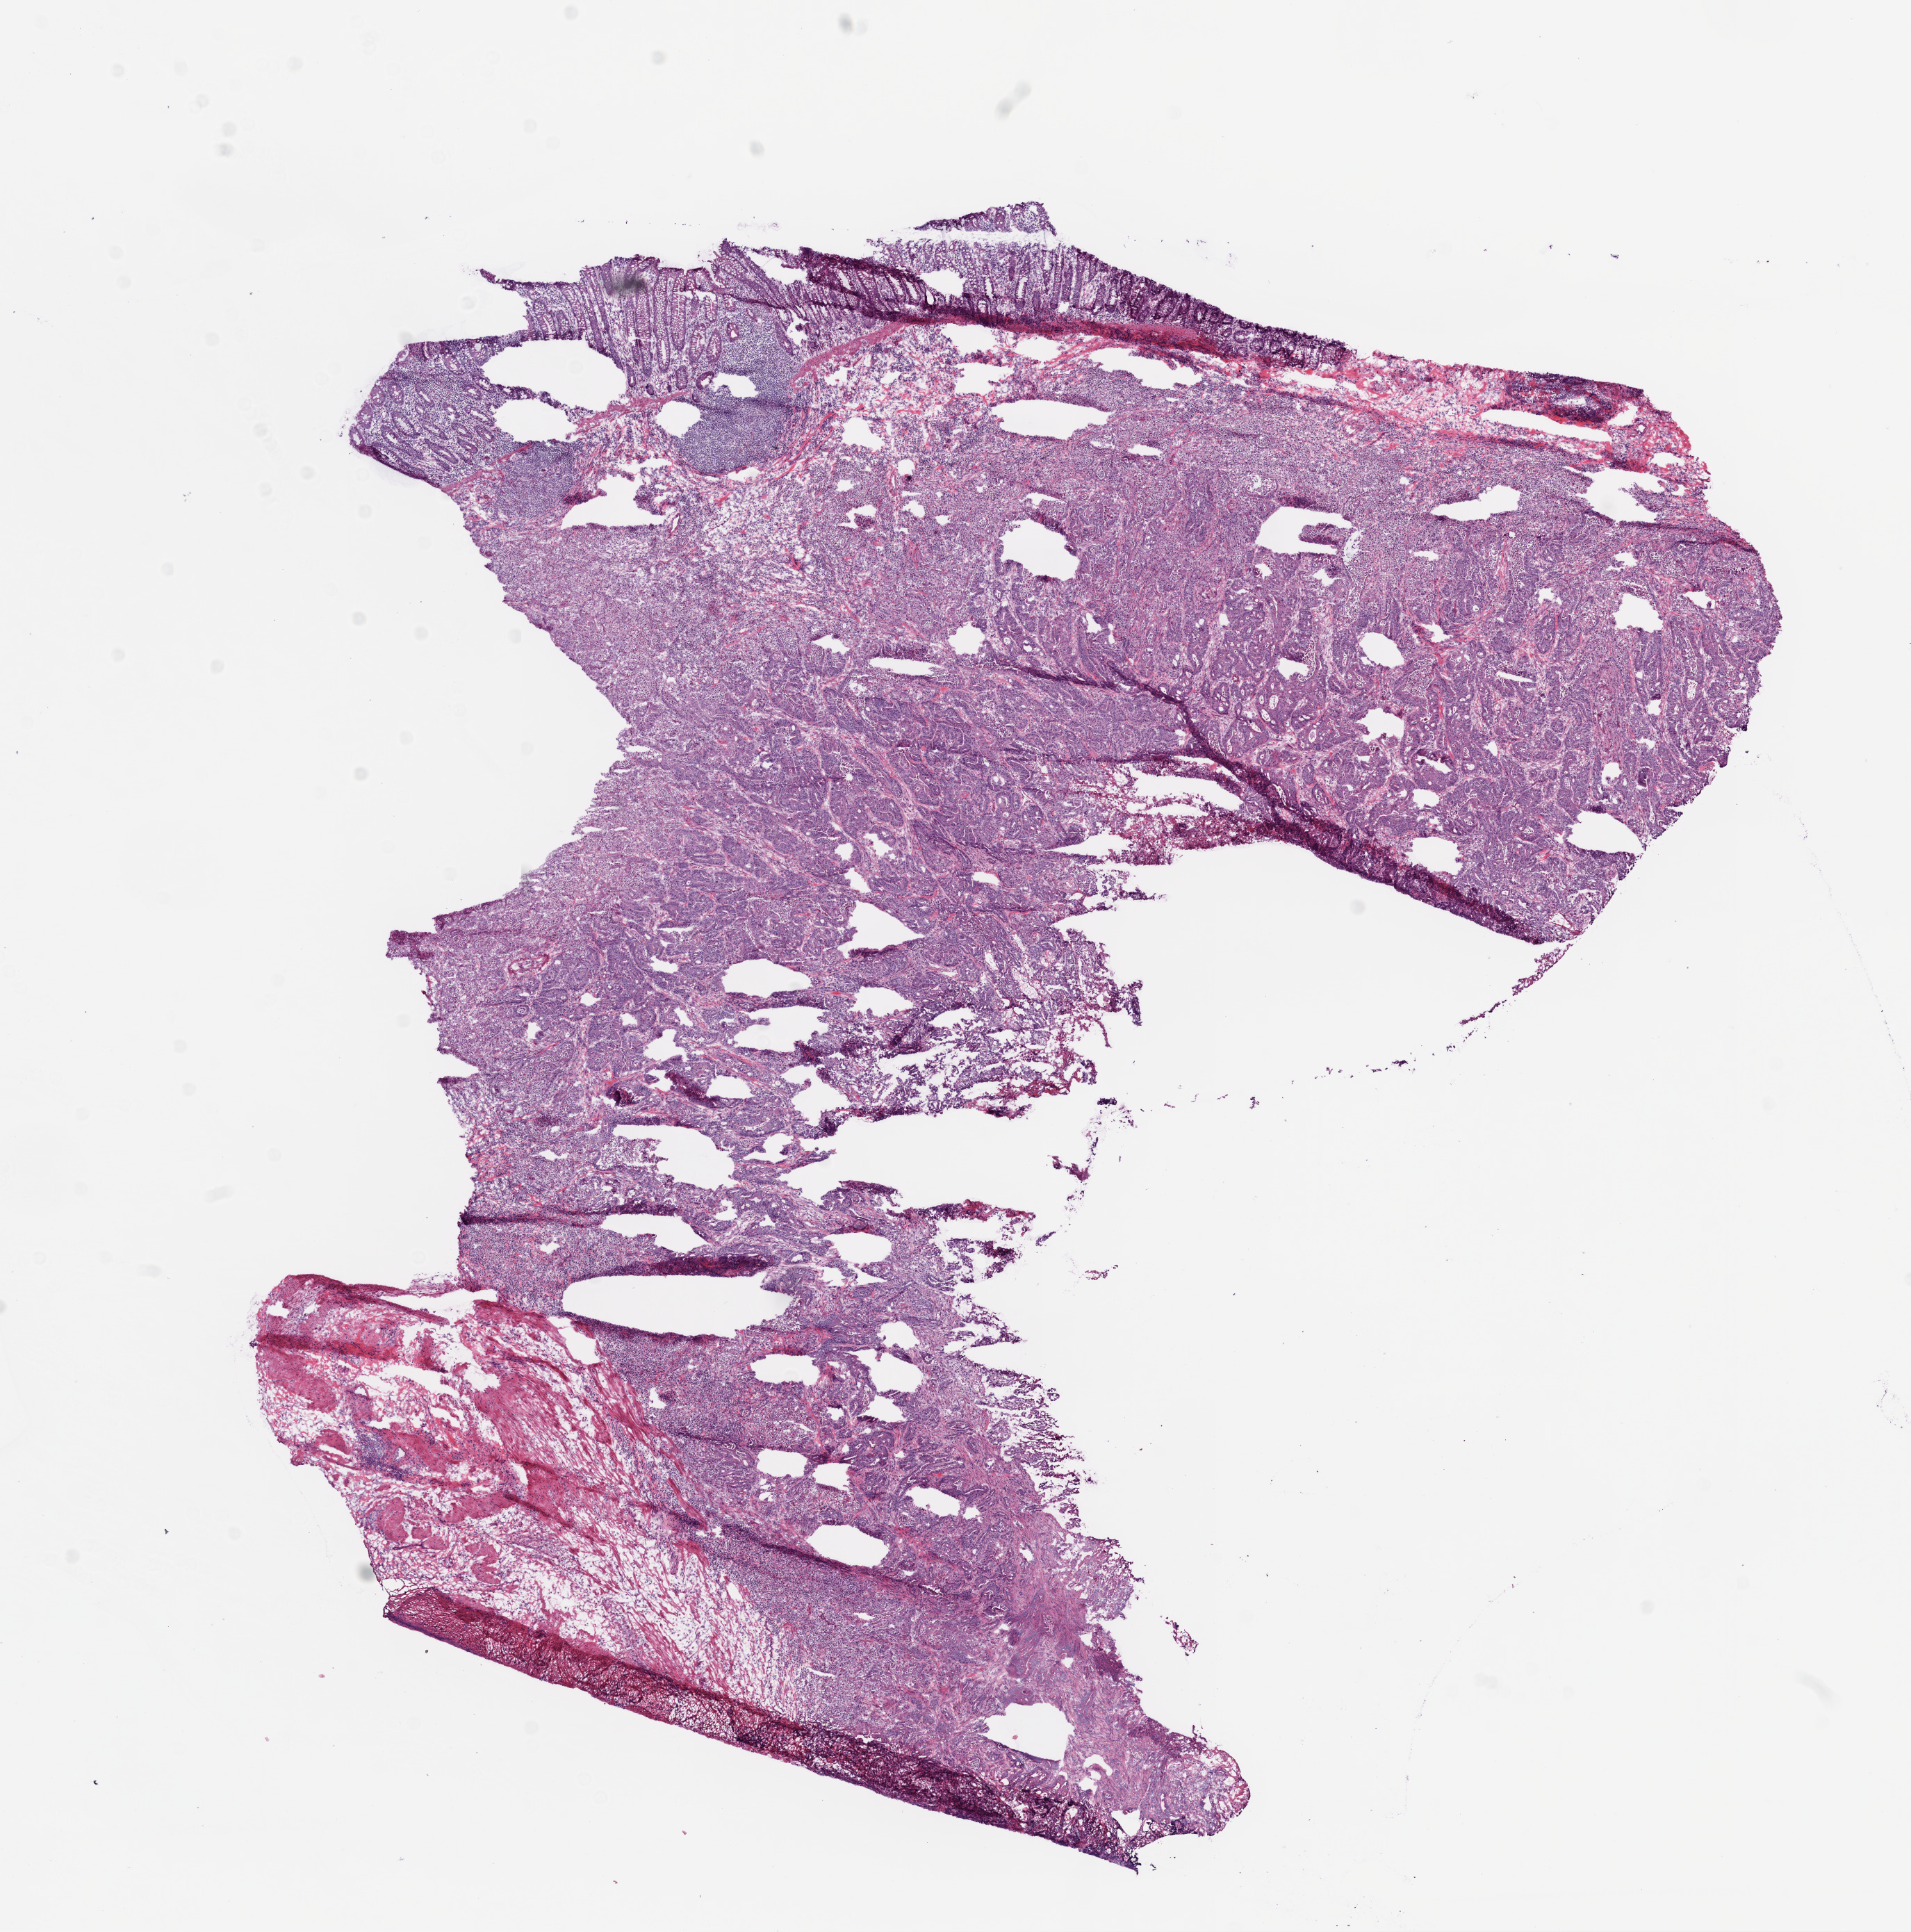
Digitized H&E tissue section (whole slide), whole scanned area (about 11.0 x 11.2 mm, from a 20x scan) shown as a low-resolution overview; frozen section from the bottom of the tissue portion; colon, primary tumour sample. Female patient; age at initial diagnosis 62 years. Pathologist review of this section (percent, as recorded): tumour cells 80%, tumour nuclei 90%, normal cells 0%, stromal cells 20%, necrosis 0%.
- diagnosis: Adenocarcinoma, NOS (ascending colon)
- TNM: T3 N0 M0
- lymph nodes positive (case pathology): 0 of 39 examined
- AJCC pathologic stage: IIA